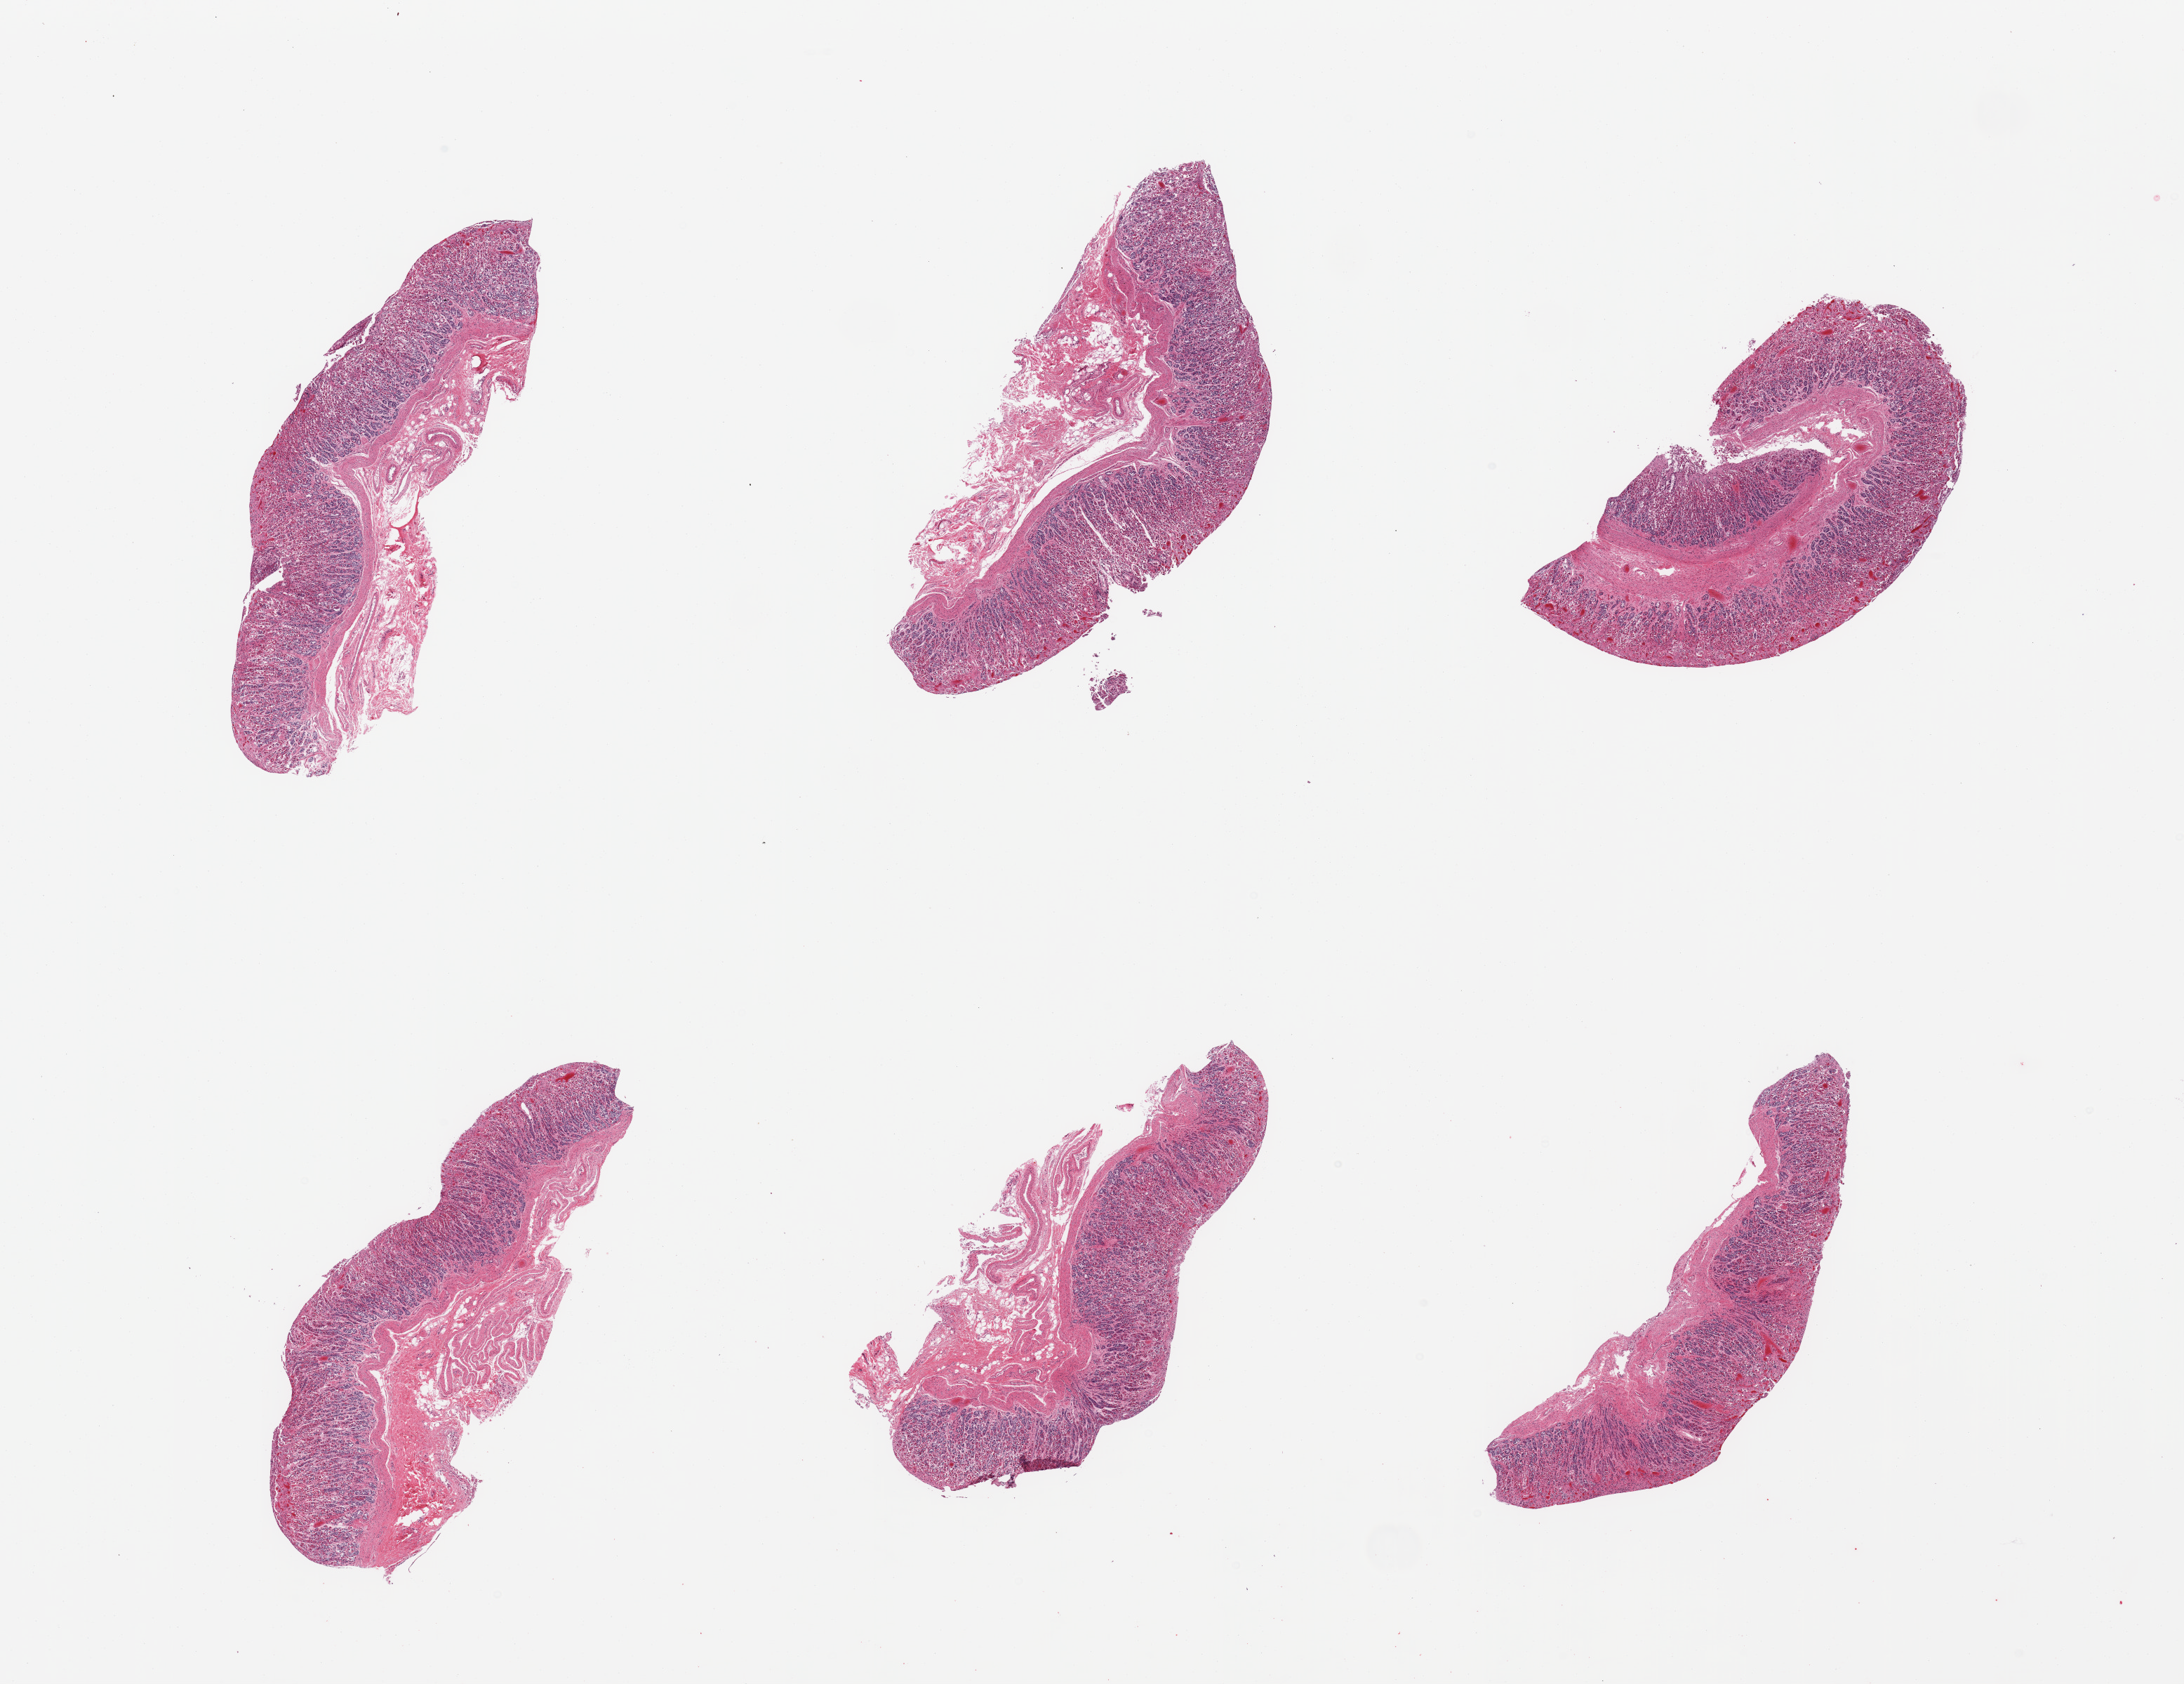
Whole-slide image, H&E stain — a low-resolution overview of the entire scanned area, about 24.6 x 19.0 mm, PAXgene-fixed paraffin-embedded (PFPE) section, sampled site (target tissue): stomach, donor tissue sample. Donor: male.
Pathologist's review note for this sample: 6 pieces; no muscularis propria present.